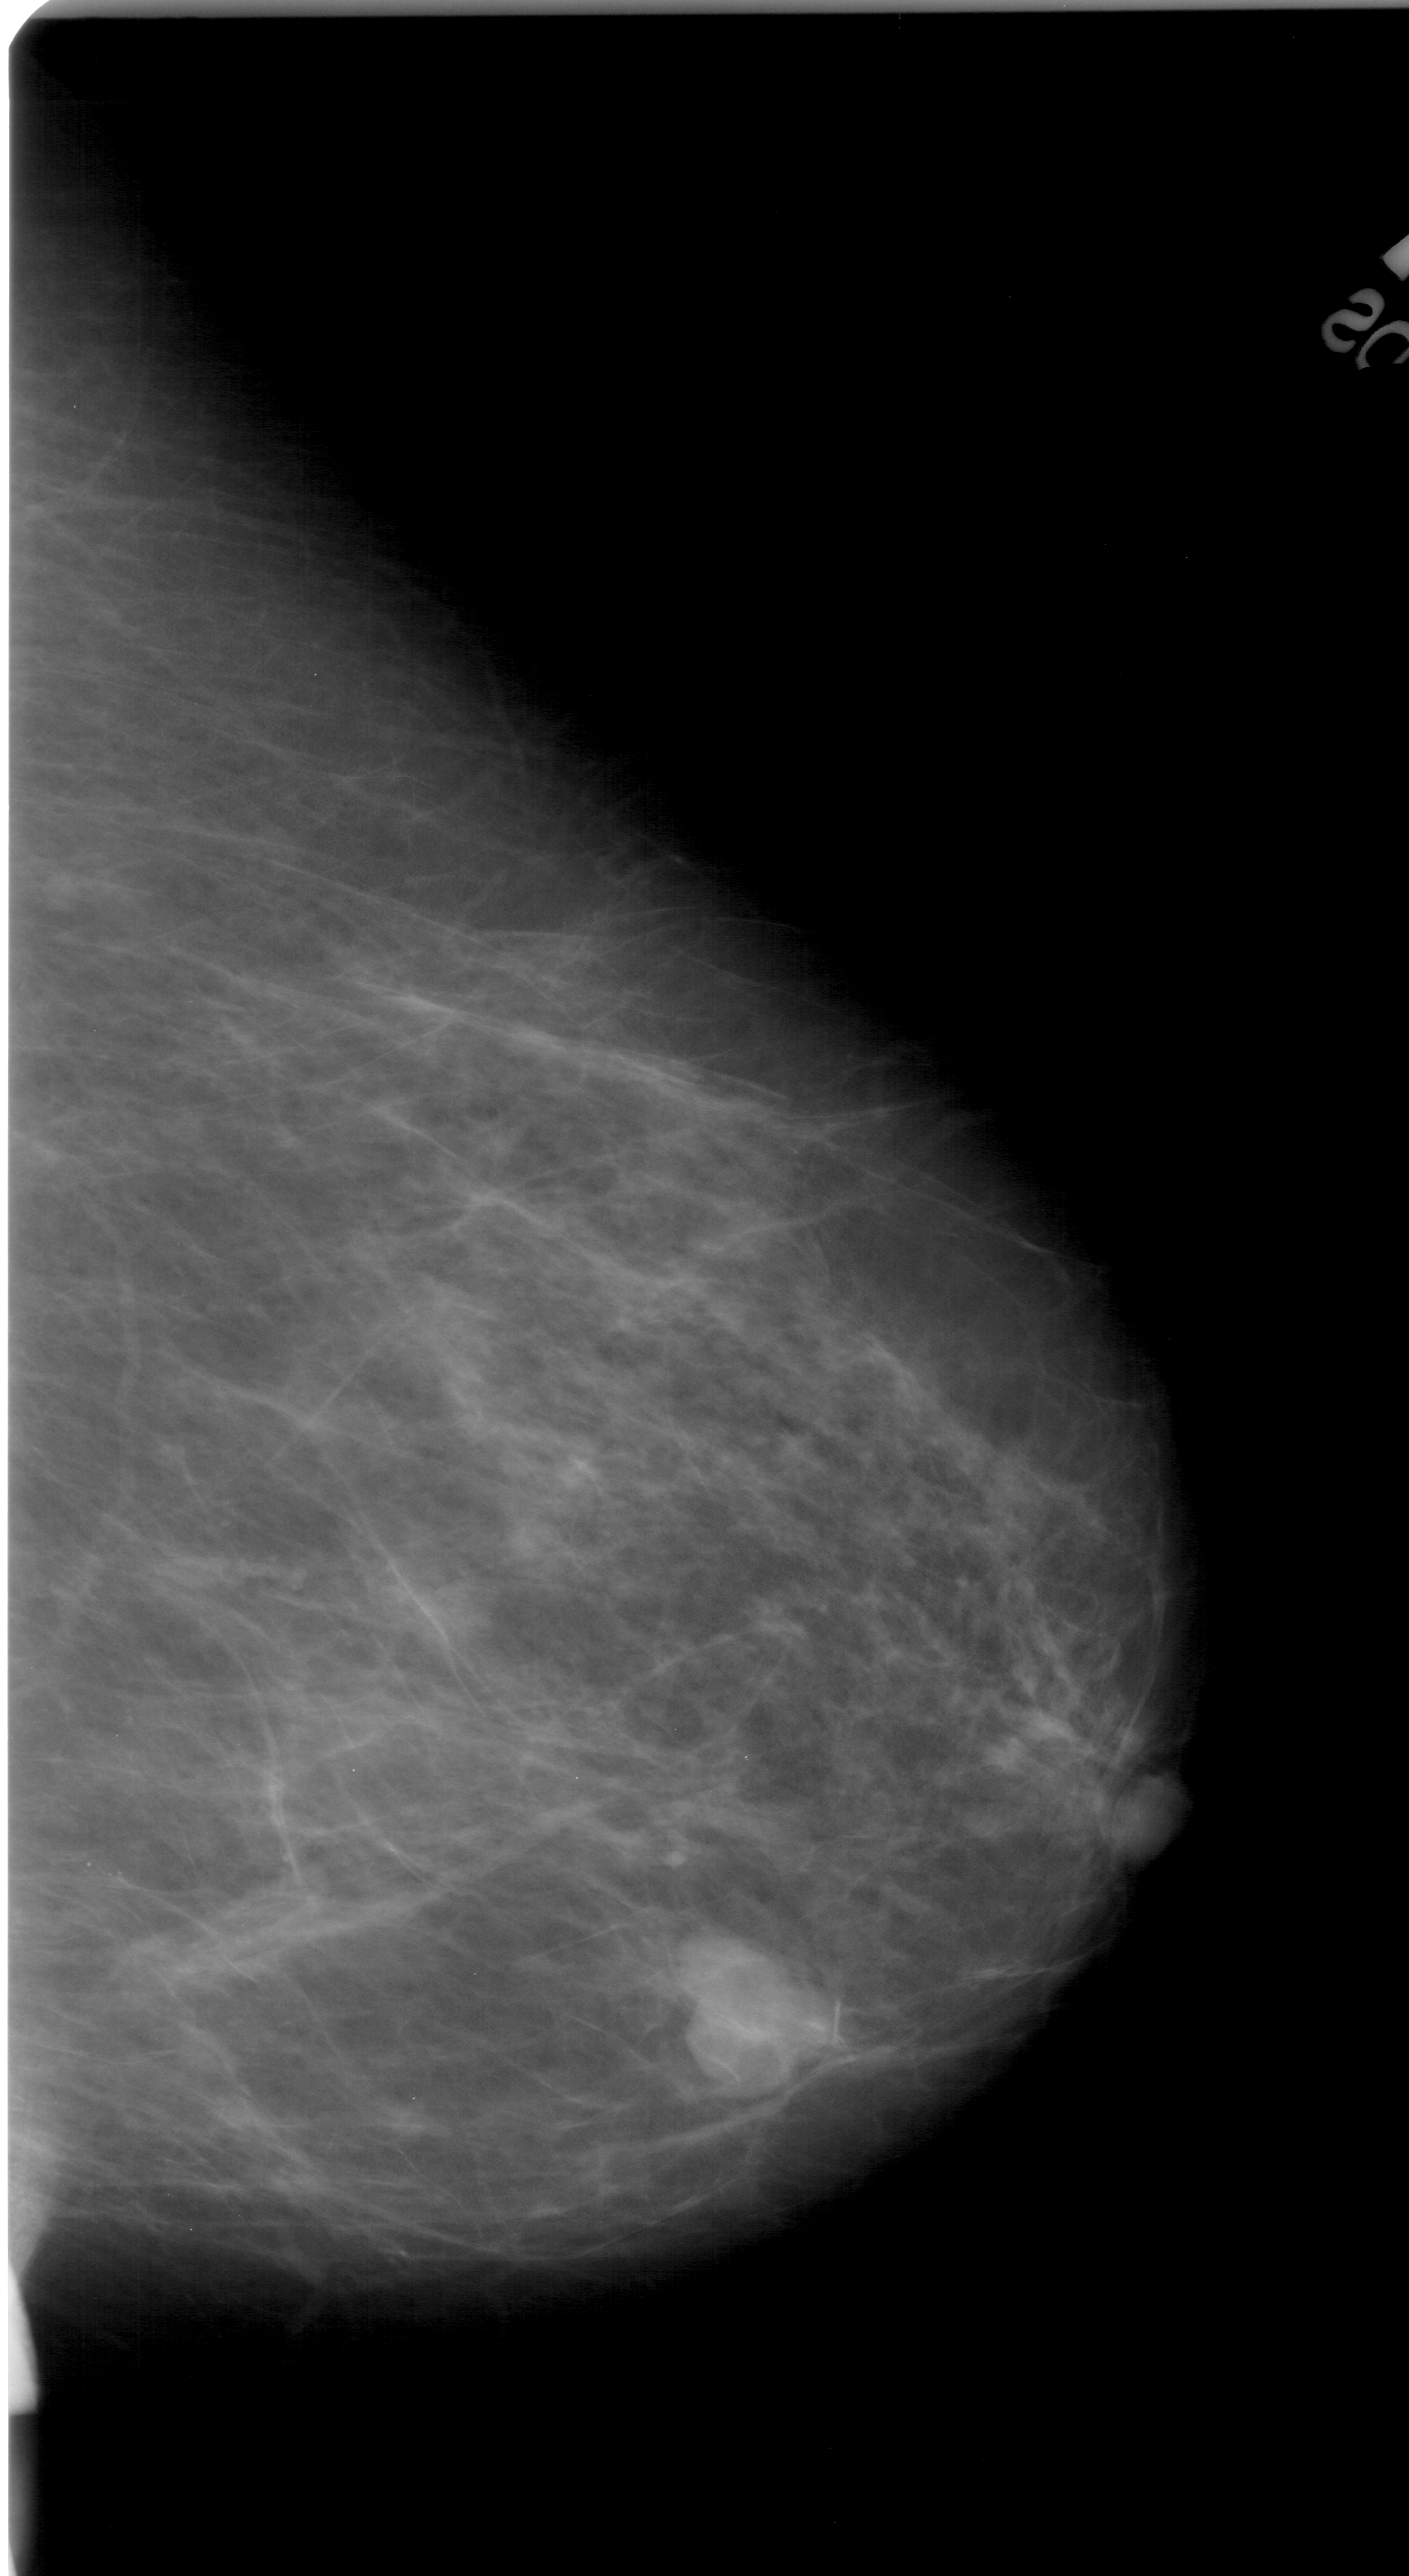
Scanned film-screen mammogram; right breast; CC view; breast composition: heterogeneously dense (BI-RADS density category 3 of 4).
Radiologist-marked abnormalities on this image: mass, shape lobulated, margins circumscribed; BI-RADS assessment category 4; pathology result (as recorded, not read from the image): benign.